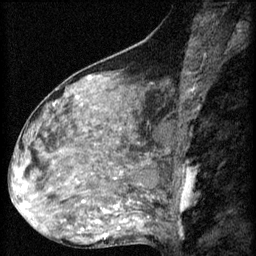
Breast MRI (dynamic contrast-enhanced), one sagittal slice; position 31 of 60 along the scan axis; 3 images stored at this slice position (order not interpretable as contrast timing); 1.5 T; TE 4.2 ms, TR 8.2 ms; 2 mm slice thickness; 256 × 256 image matrix, field of view 180 × 180 mm. Patient: female, 48 years.
Structures marked on this image (semi-automatically segmented with operator editing):
- analysis volume of interest (the breast-tissue region the enhancement analysis was run in; not a lesion): bounding box [x1, y1, x2, y2] px = [48, 160, 125, 217]
- tumour enhancement mask (voxels above the 70 % enhancement threshold inside the analysis volume of interest): [82, 200, 119, 207]